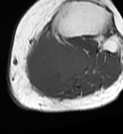
MRI of an extremity soft-tissue mass, one axial slice. Position 41 of 68 along the scan axis. MR volume resampled by the dataset authors to the PET/CT grid (not the native acquisition matrix). 3.27 mm slice thickness. 123 × 134 image matrix, field of view 120 × 131 mm. Female patient. Case-level facts recorded for this patient, not image findings: histological type: extraskeletal high grade osteogenic sarcoma; grade: high; site of the primary tumour: left calf.
Outlined on this slice (expert contour drawn on MRI and transferred to this co-registered scan by the dataset authors):
- gross tumour volume (mass): box from (x=24, y=32) to (x=89, y=92) px